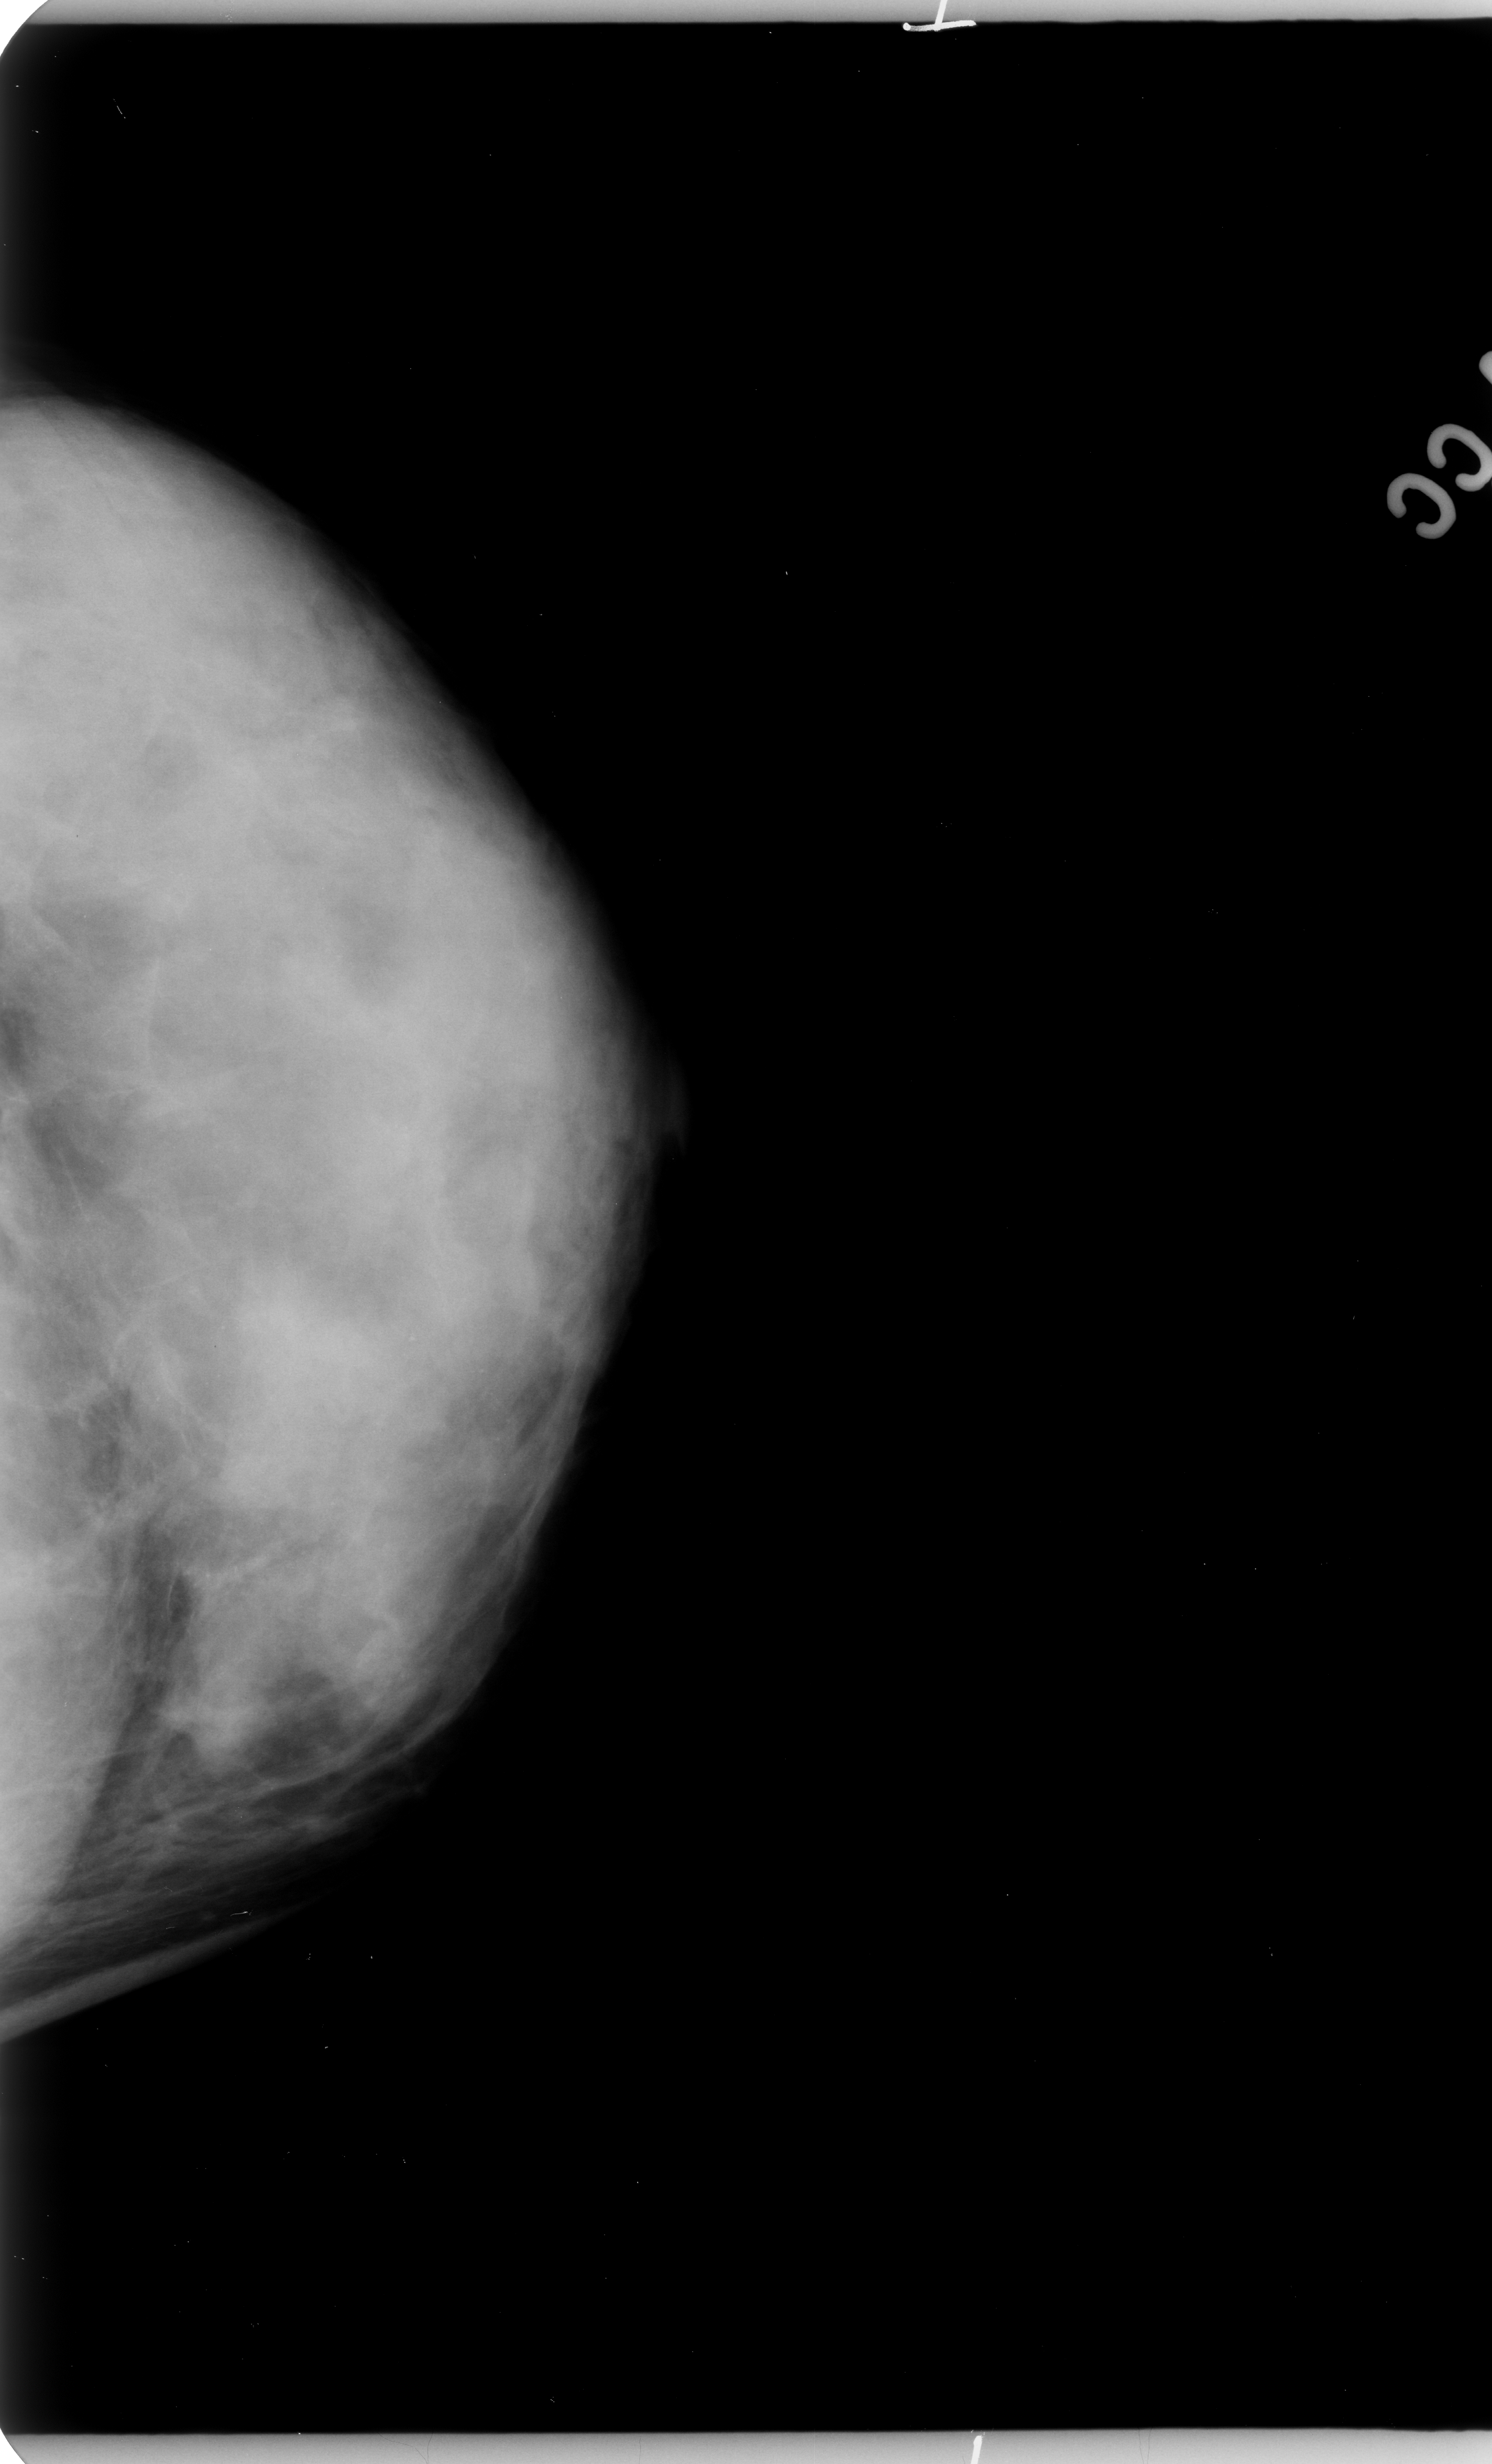
Scanned film-screen mammogram; left breast; craniocaudal (CC) view; BI-RADS breast density category 4 (scale 1–4).
Marked abnormality: calcifications, morphology pleomorphic, distribution regional; BI-RADS assessment category 4; pathology result (as recorded, not read from the image): malignant.